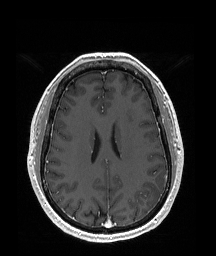
Brain MRI from a brain-tumour surgery series, one axial slice; slice 78 of 192 in the series (ordered by position); T1-weighted post-contrast; 216 × 256 image matrix. From the clinical record (not read from this slice): histopathology: Glioblastoma; WHO grade: 4; IDH mutation: no; tumour location: Left Temporal Parietal.
Structures marked on this image (manually delineated by an expert):
- tumour: bounding box [x1, y1, x2, y2] px = [142, 181, 164, 208]